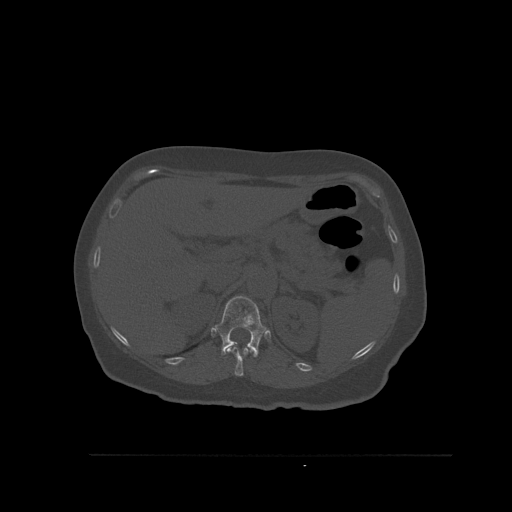
CT including the spine, one axial slice; position 291 of 527 along the scan axis; bone window (W 1800 / L 400 HU); 1.5 mm slice thickness; 512 × 512 image matrix, field of view 470 × 470 mm. Patient: female, 73 years. From the clinical record (not read from this slice): primary cancer: breast; vertebrae with lytic lesions (as recorded): L2.
Annotated regions visible in this slice (semi-automatically segmented with operator editing):
- T11 vertebra: box from (x=222, y=346) to (x=252, y=376) px
- T12 vertebra: (x=214, y=296)–(x=268, y=358)